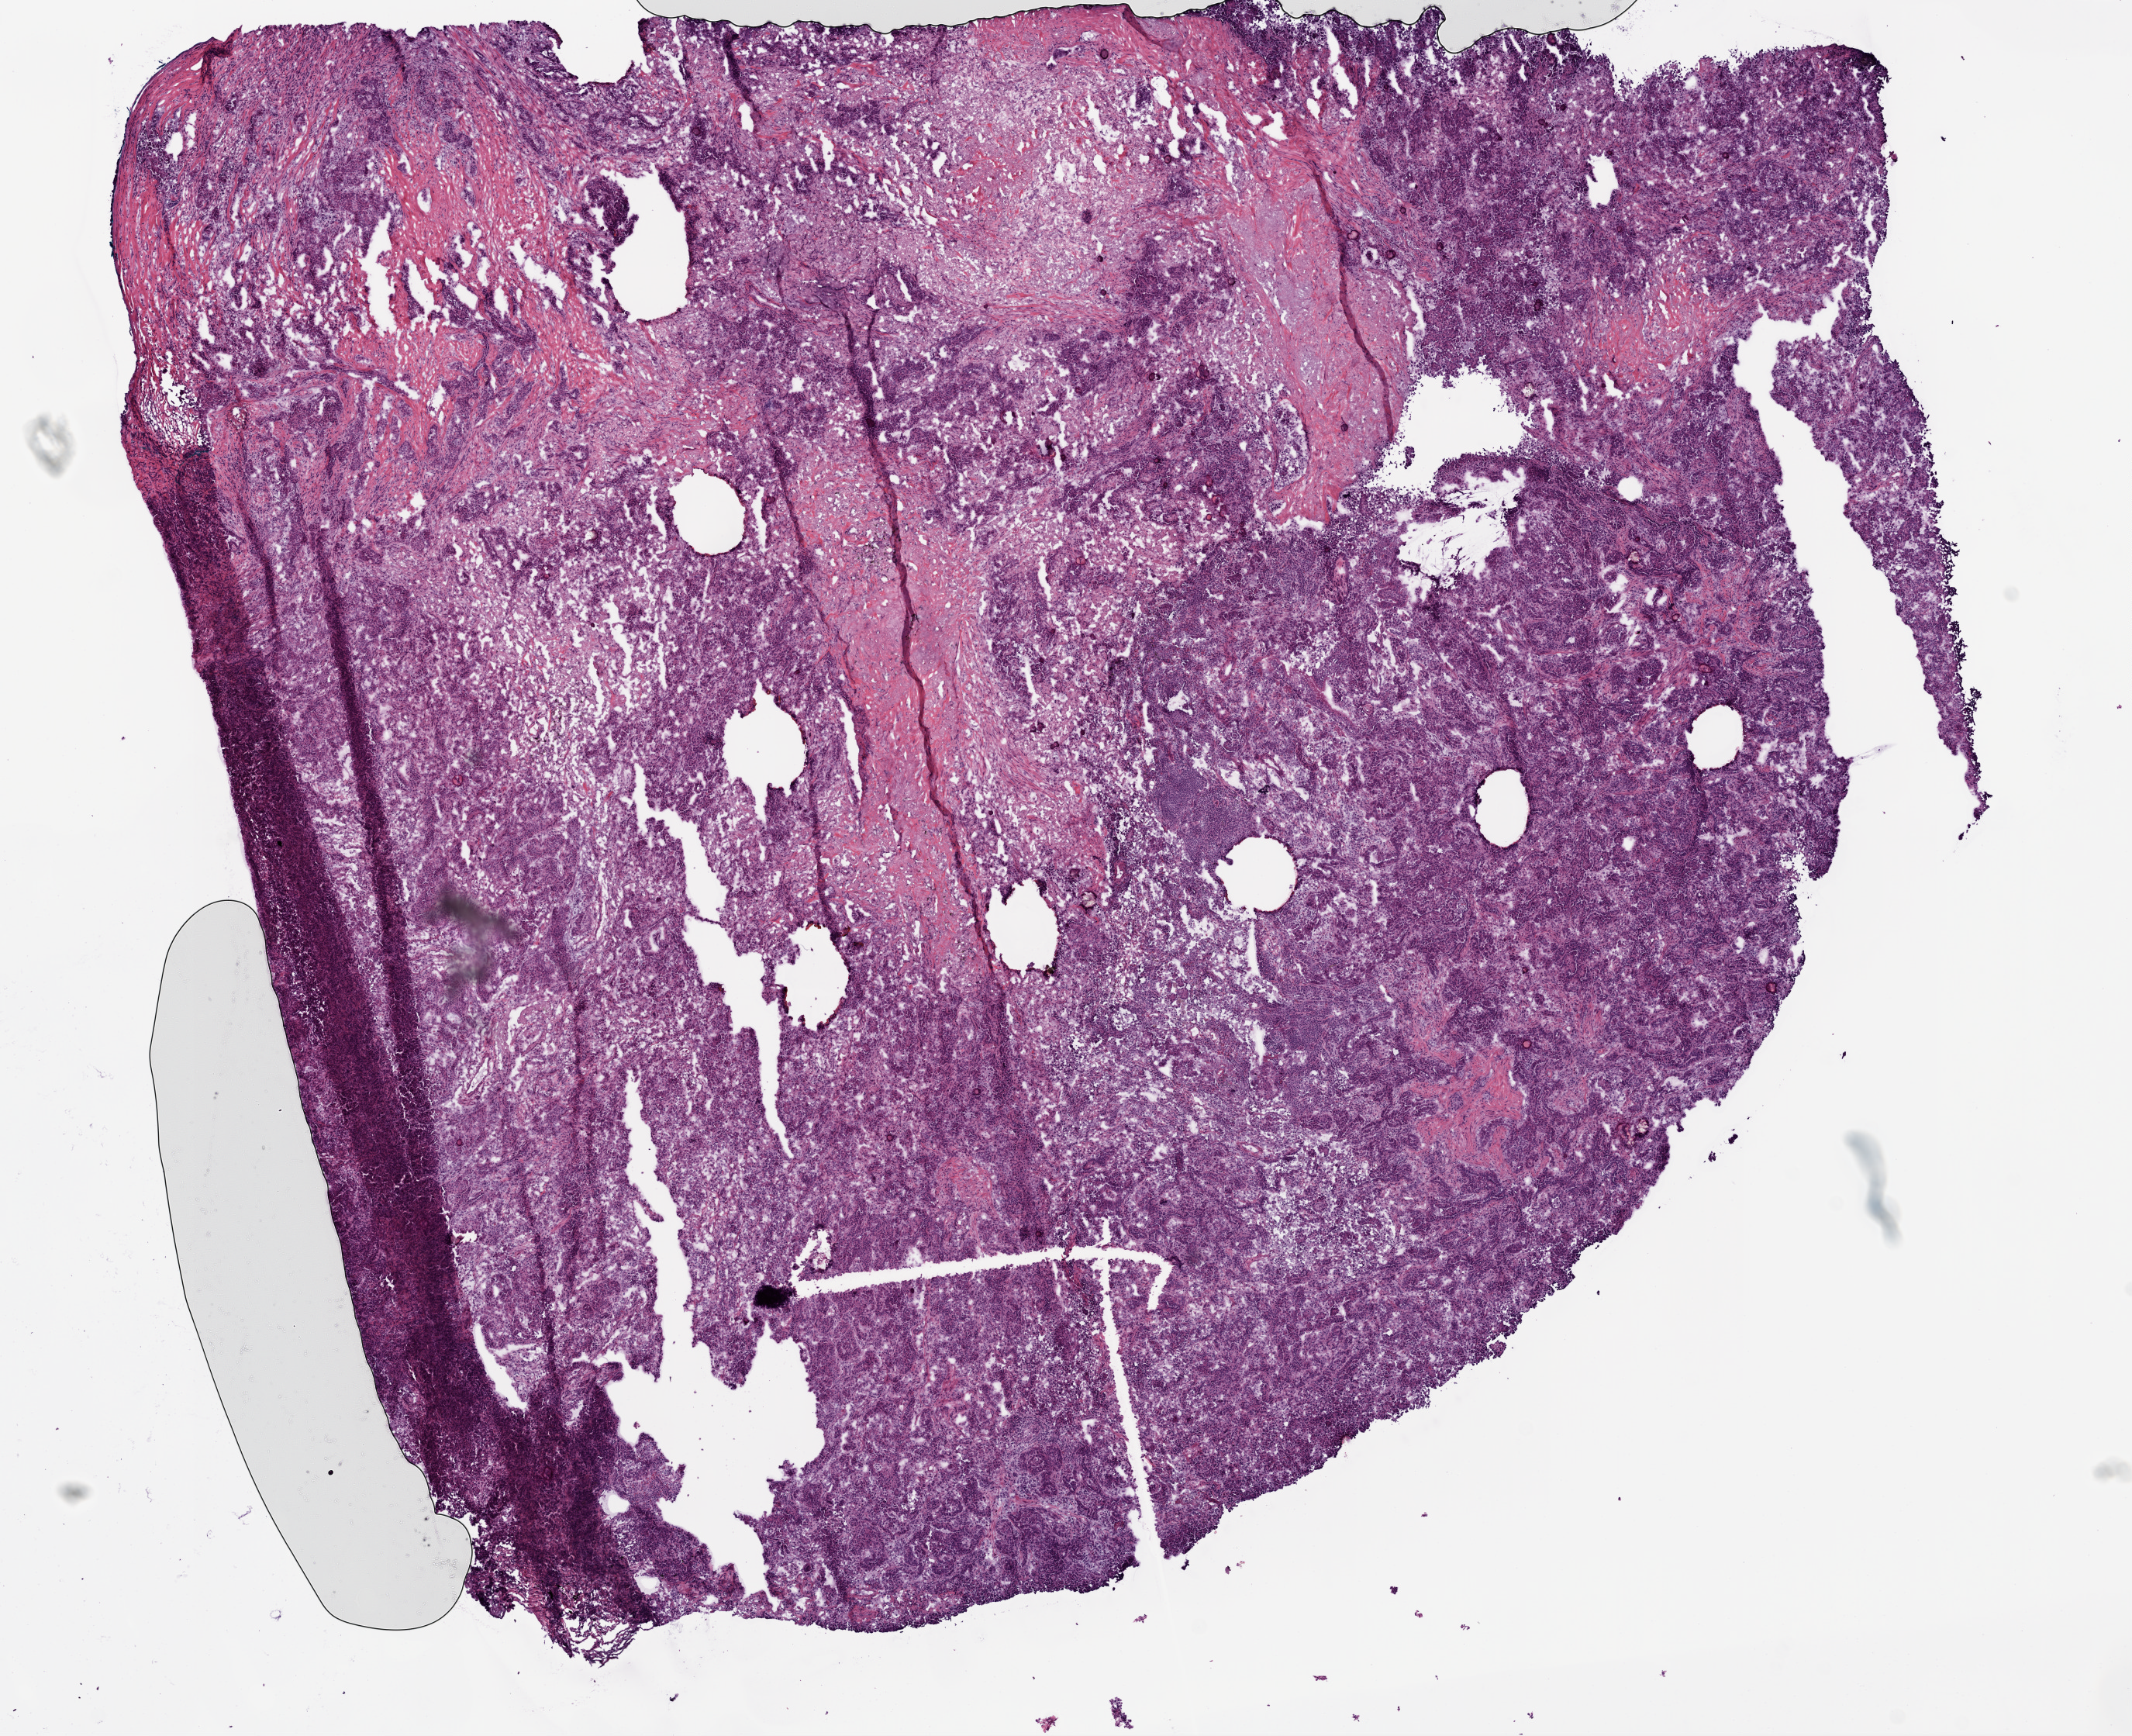
Digitized Hematoxylin and eosin (H&E) stained tissue section (whole slide) — shown as a low-resolution overview of the whole scanned area (about 11.0 x 9.0 mm), frozen section from the top of the tissue portion, lung, primary tumour sample. Patient: female, age at initial diagnosis 42 years.
Diagnosis: Adenocarcinoma with mixed subtypes (lower lobe, lung).